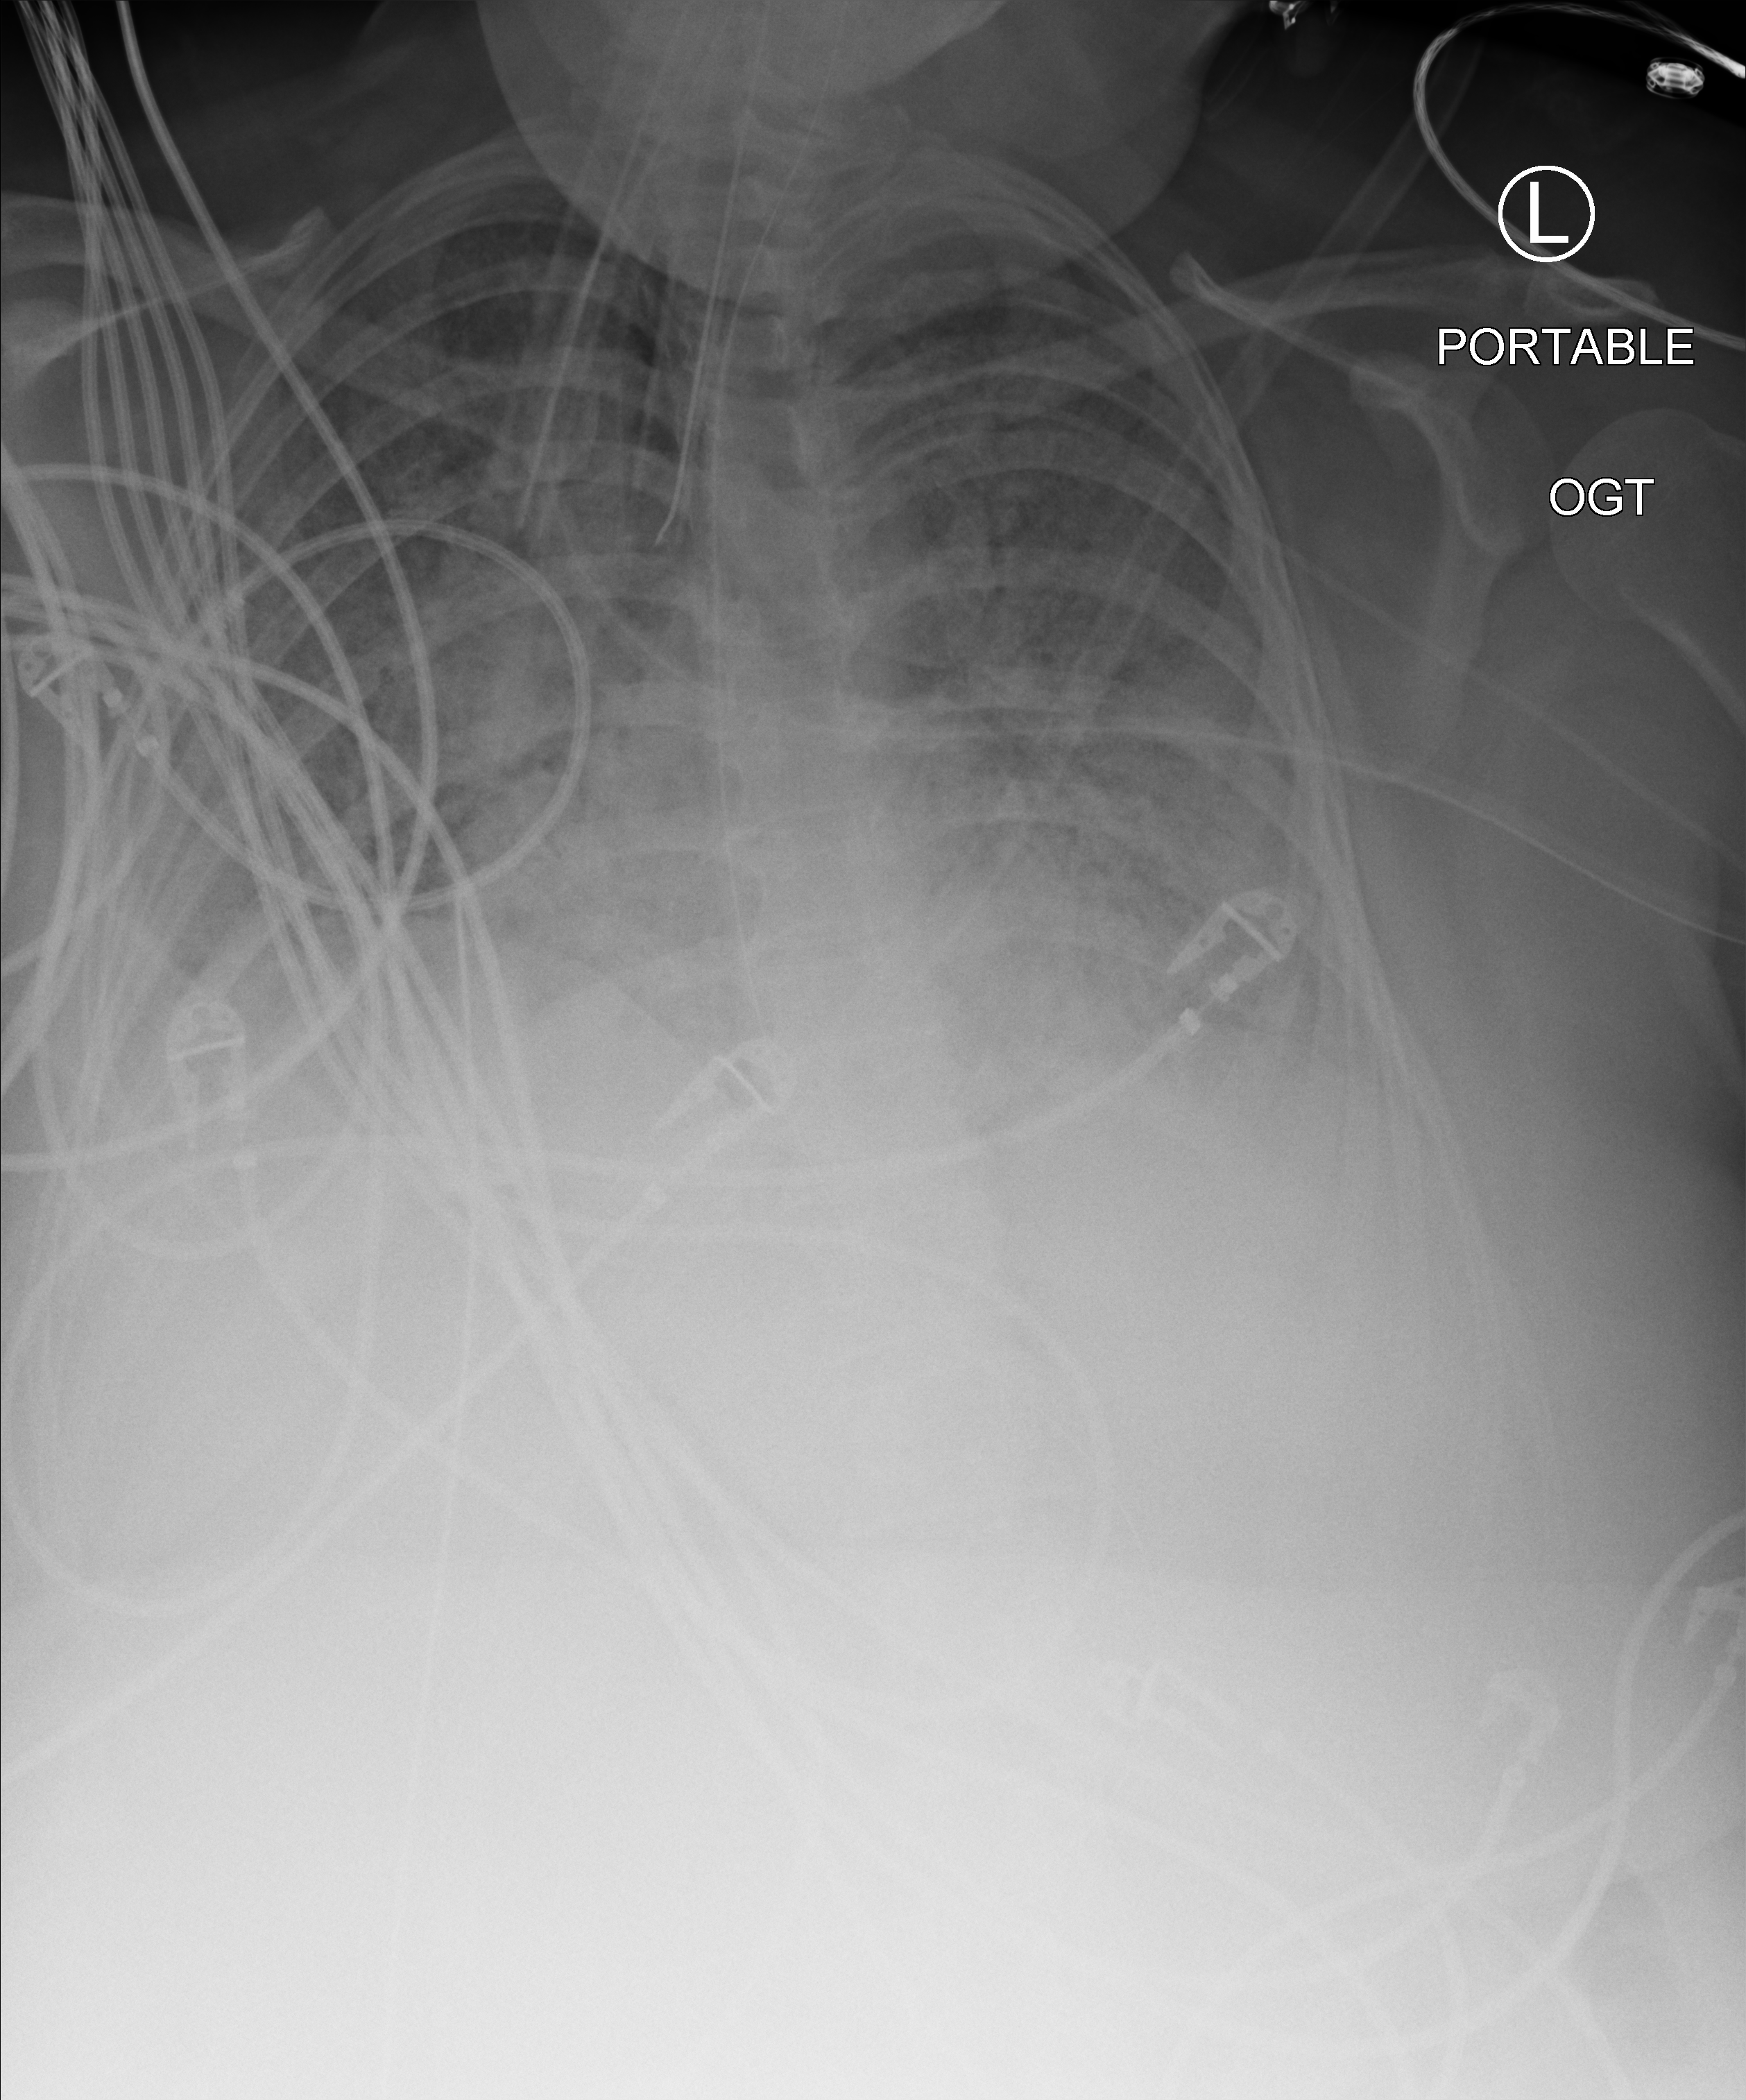
Portable chest radiograph, anteroposterior (AP) projection. Patient hospitalised with COVID-19; female, aged 18–59 years.
From the hospital-stay record, not from the radiograph (when in the stay this image was taken is not recorded): COPD (admission record): no; admitted to intensive care during this hospital stay: yes; smoking status (admission record): never.